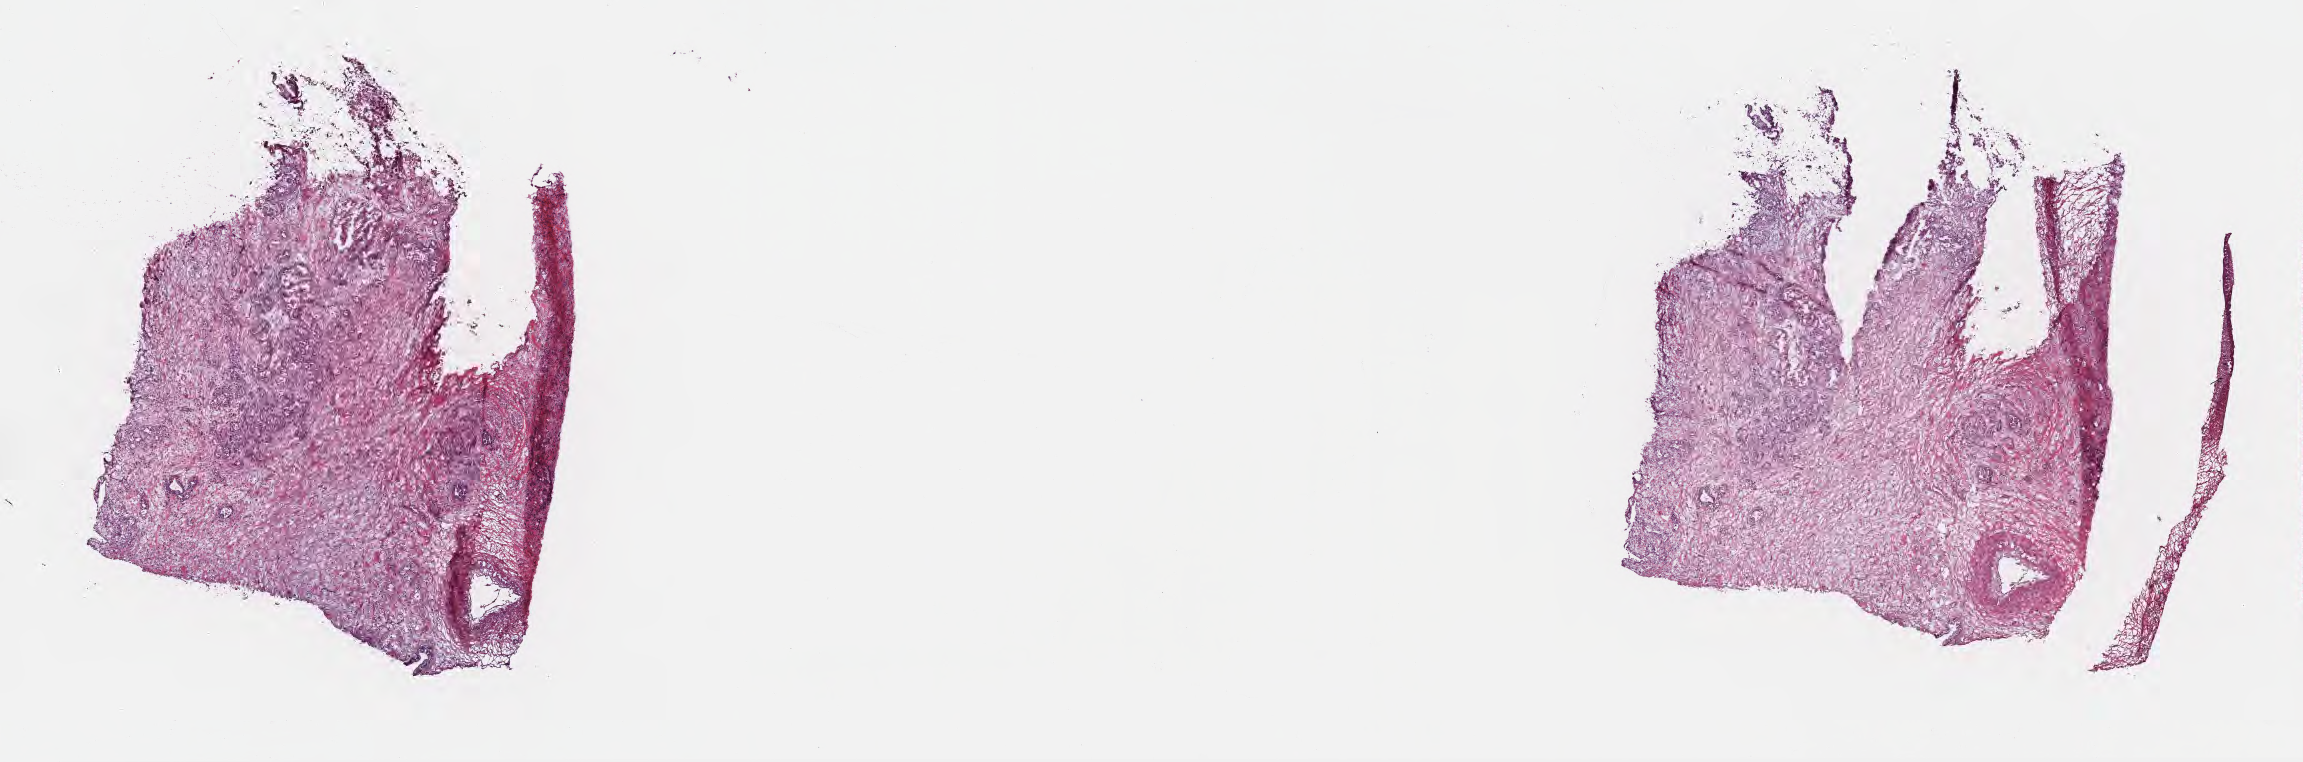
Digitized H&E-stained section, low-resolution overview of the scanned area, about 18.6 x 6.2 mm. Frozen section. Primary tumor. Anatomic site: head of pancreas. Female, age 73 years at initial diagnosis. Tumor grade: G2 (moderately differentiated). Pathologist review of this section (percent, as recorded): tumor cells 20%, tumor nuclei 80%, stromal cells 75%, necrosis 0%, normal cells 5%. Infiltration values recorded for this section: lymphocyte infiltration 0%, monocyte infiltration 0%, neutrophil infiltration 0%.
- diagnosis: Infiltrating duct carcinoma, NOS
- AJCC pathologic stage: Stage III